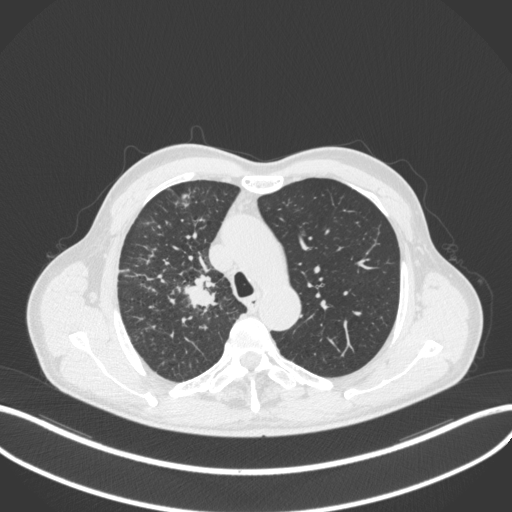
Chest CT, one axial slice; slice 354 of 490 in the series (ordered by position); 120 kVp; lung window (W 1500 / L -600 HU); 1 mm slice thickness; 512 × 512 image matrix, field of view 400 × 400 mm. Patient: male, 69 years. From the clinical record (not read from this slice): clinical TNM (as recorded): T2a N0 M0.
Annotated regions visible in this slice (rectangle marked by the reading radiologist):
- lung tumour (recorded histology: adenocarcinoma): bounding box <176,268,224,316> (left, top, right, bottom; pixels)